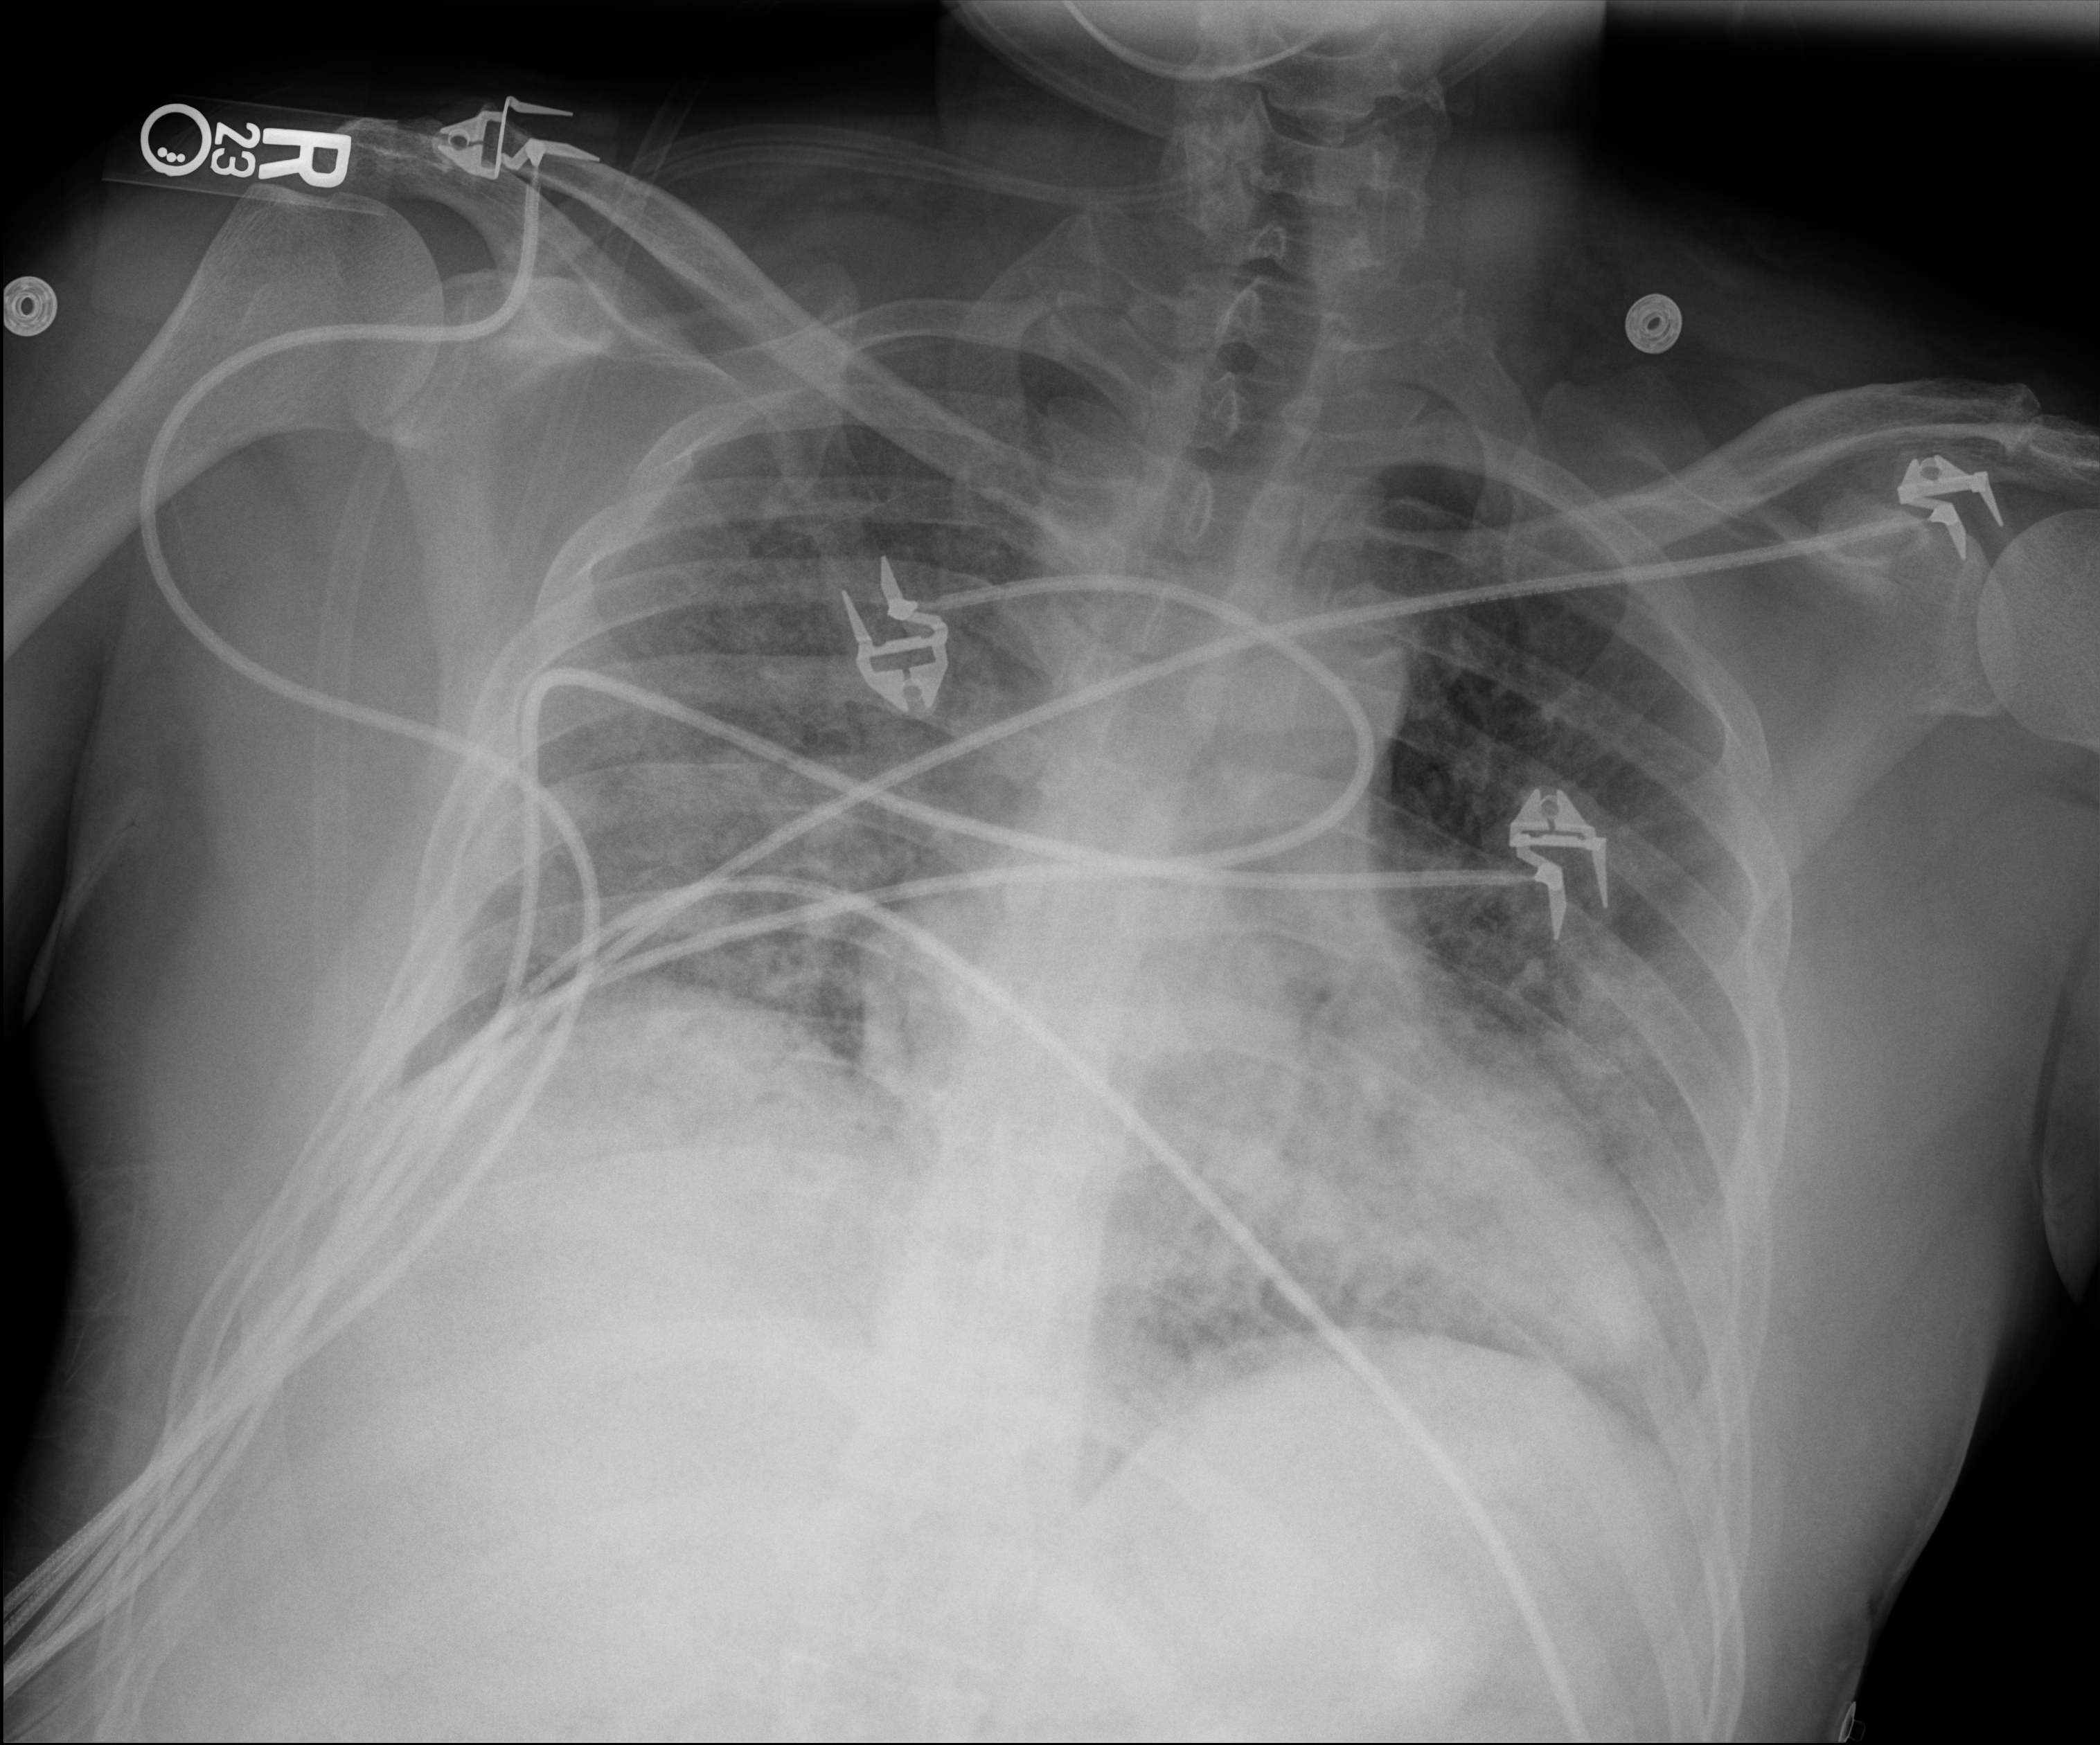
Chest X-ray (portable). Patient hospitalised with COVID-19; male, aged 18–59 years.
From the hospital-stay record, not from the radiograph (when in the stay this image was taken is not recorded):
- smoking status (admission record): never
- mechanically ventilated during this hospital stay: no